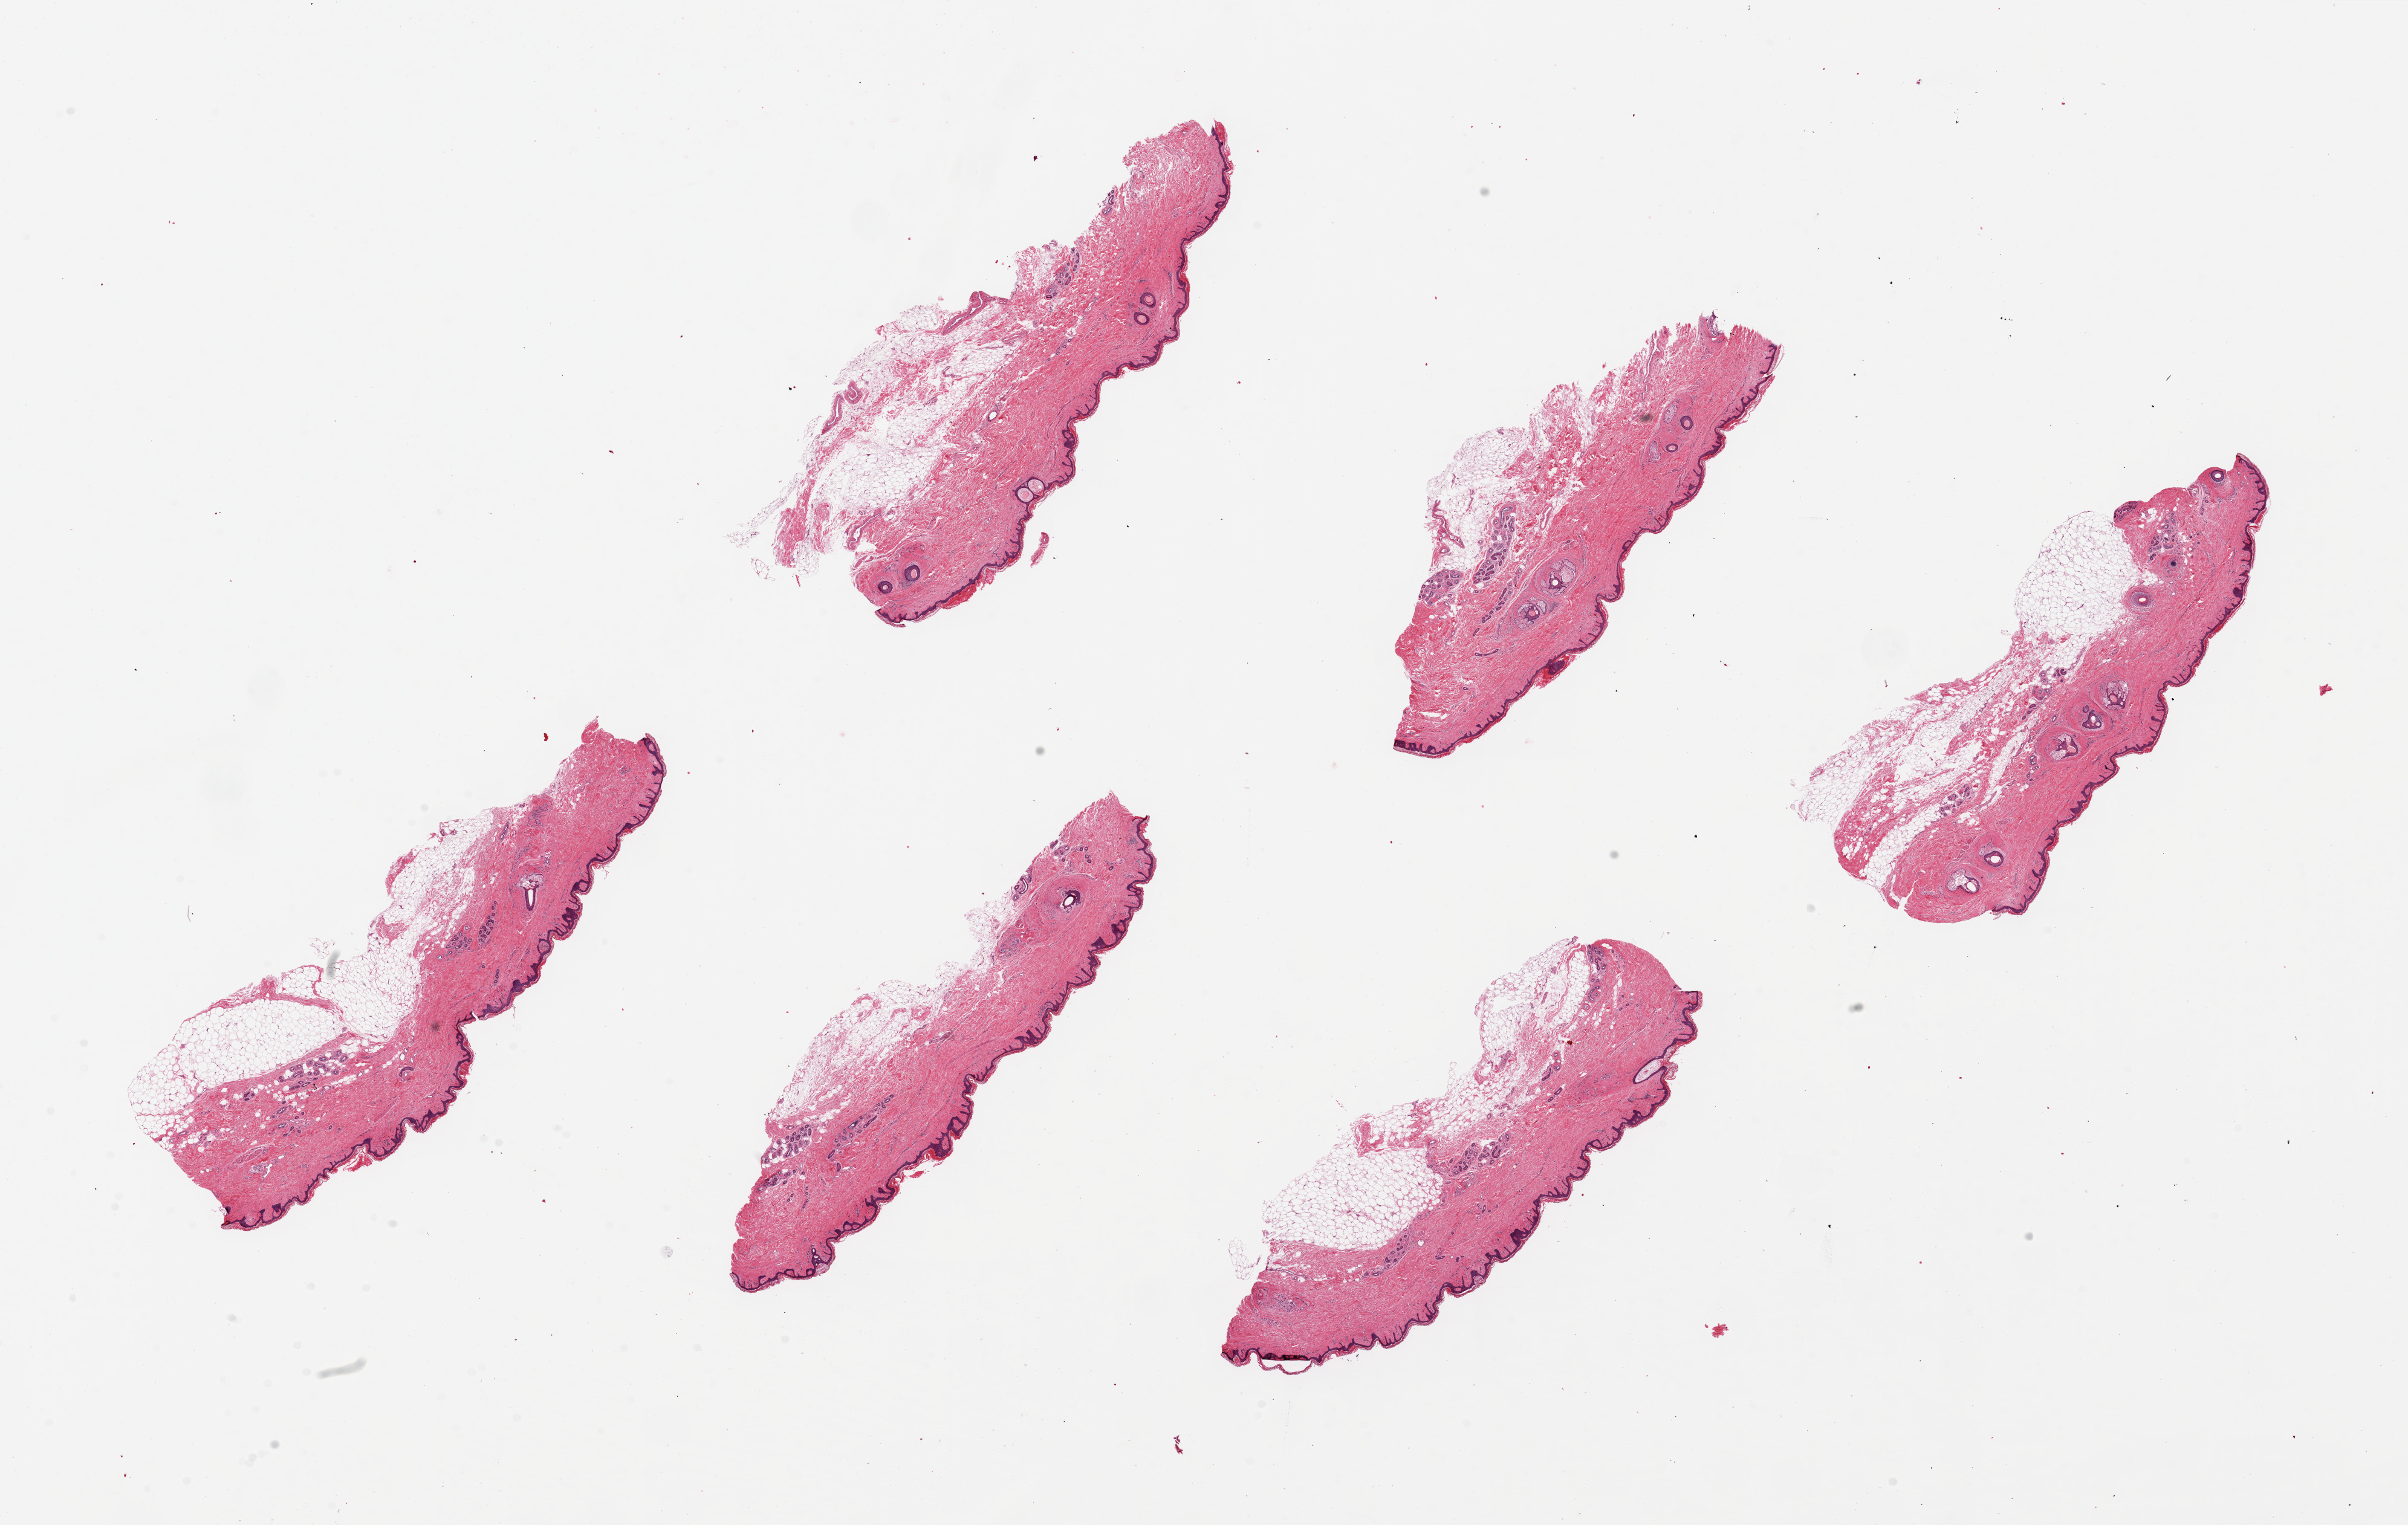
Haematoxylin and eosin whole-slide image, brightfield, a low-resolution overview of the entire scanned area, about 31.5 x 20.0 mm; PAXgene-fixed paraffin-embedded (PFPE) section; section of skin of suprapubic region (target tissue); tissue donor sample.
Pathologist's review note for this sample: 6 pieces, up to 8.5x3mm; all have up to 1.5 mm subcutaneous adipose.